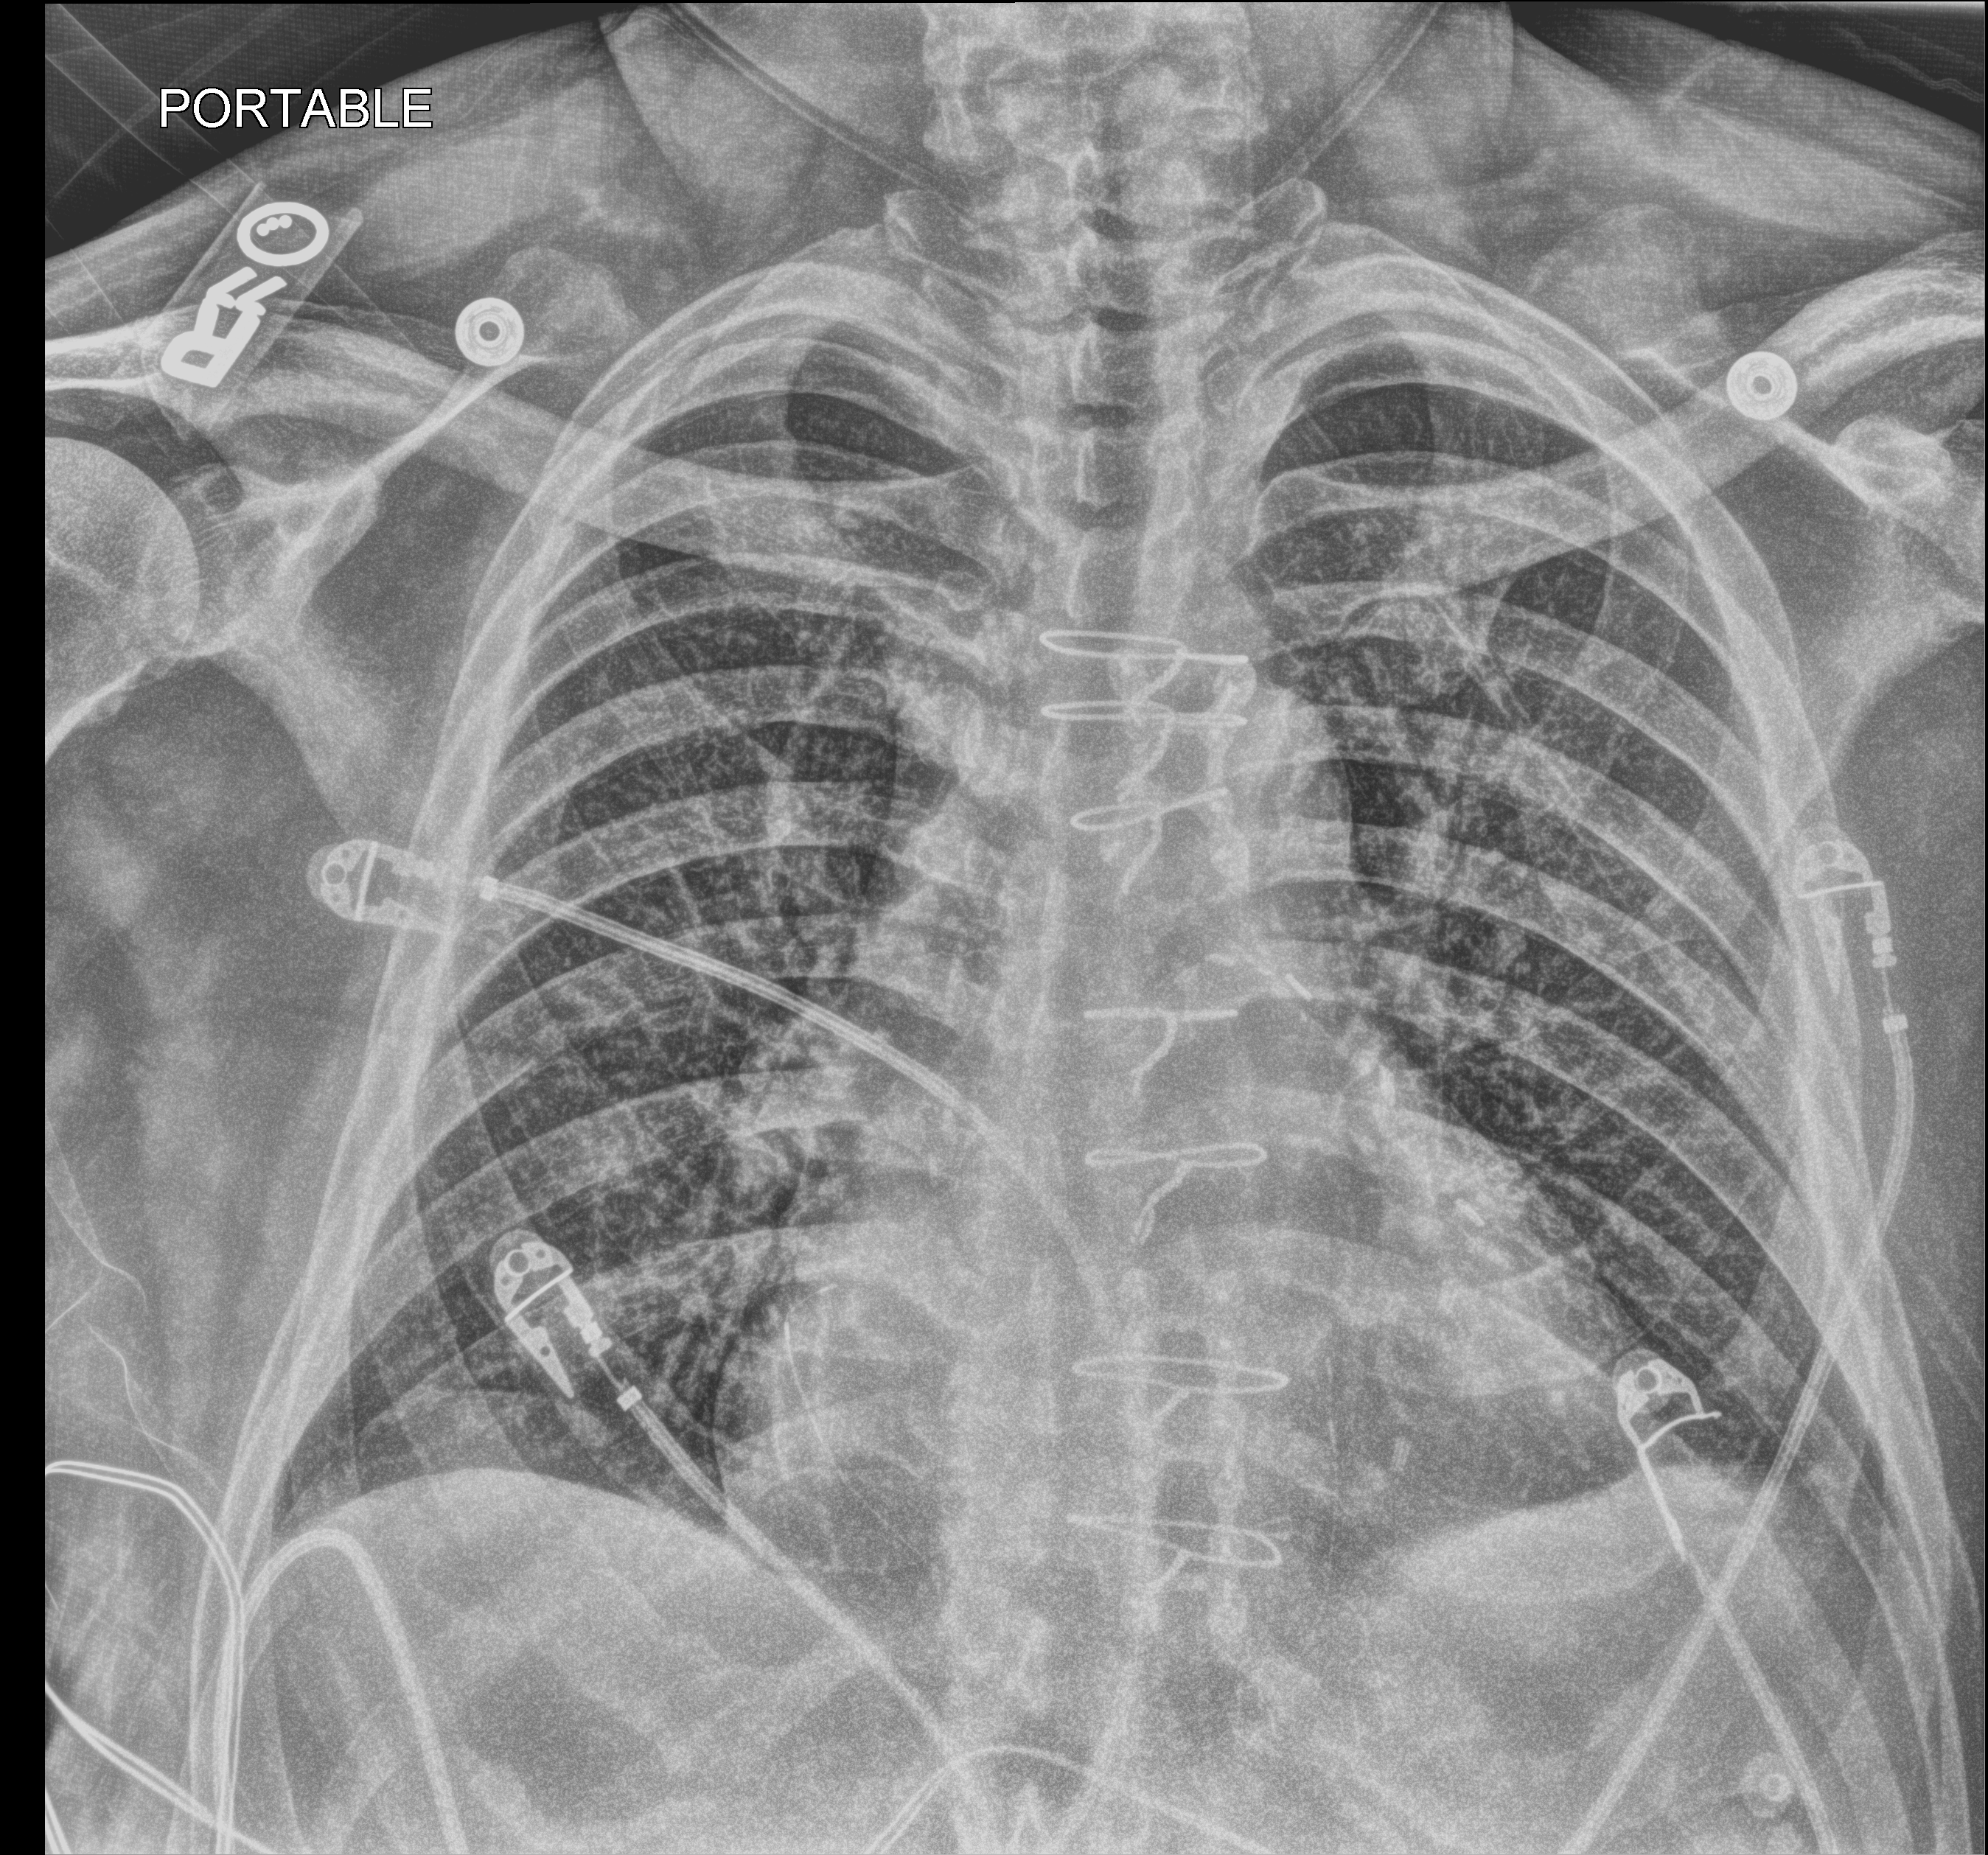
Portable chest radiograph, anteroposterior (AP) projection. Male patient hospitalised with COVID-19, age 60–74 years.
From the hospital-stay record, not from the radiograph (when in the stay this image was taken is not recorded): admitted to intensive care during this hospital stay: no.